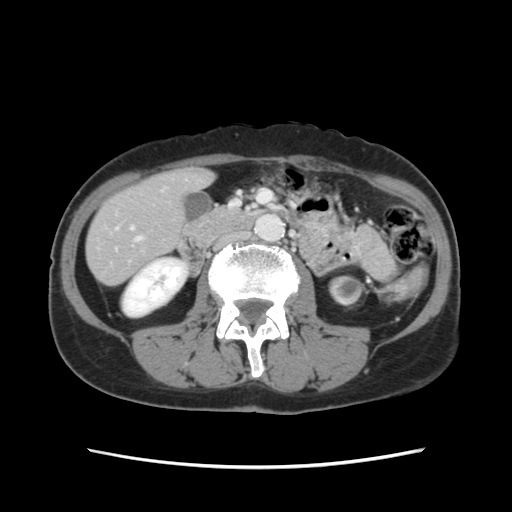
Contrast-enhanced abdominal CT, one axial slice; position 29 of 120 along the scan axis; soft-tissue window (W 400 / L 40 HU); 2.5 mm slice thickness; 512 × 512 image matrix, field of view 330 × 330 mm. Female patient, age 70 years. Case-level facts recorded for this patient, not image findings: diagnosis: colorectal cancer liver metastases, imaged before liver resection; multiple liver metastases: no; largest metastasis: 2.5 cm; chemotherapy before resection: yes.
Annotated regions visible in this slice (expert manual segmentation):
- hepatic veins: box from (x=136, y=237) to (x=141, y=241) px
- liver: (x=88, y=171)–(x=210, y=284)
- planned liver remnant (the part of the liver to remain after resection): (x=88, y=171)–(x=208, y=285)
- portal vein (with intrahepatic branches): (x=130, y=227)–(x=134, y=230)